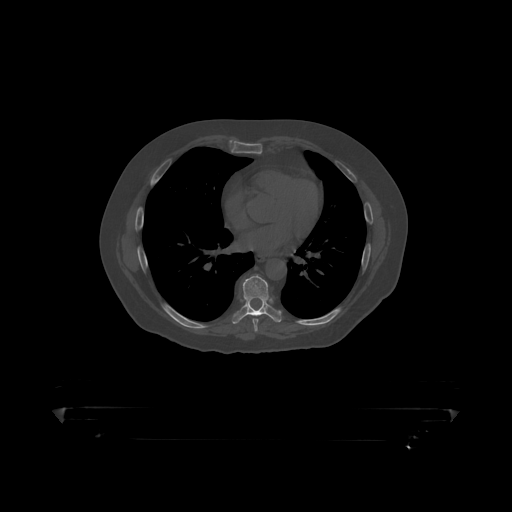
CT including the spine, one axial slice. Position 262 of 390 along the scan axis. 120 kVp. Bone window (W 1800 / L 400 HU). 512 × 512 image matrix, field of view 650 × 650 mm. Patient: male, 60 years. From the clinical record (not read from this slice): primary cancer: prostate.
Outlined on this slice (semi-automatic segmentation, software-assisted and operator-edited):
- T8 vertebra: bounding box (x1, y1, x2, y2) in pixels: (234, 276, 282, 318)